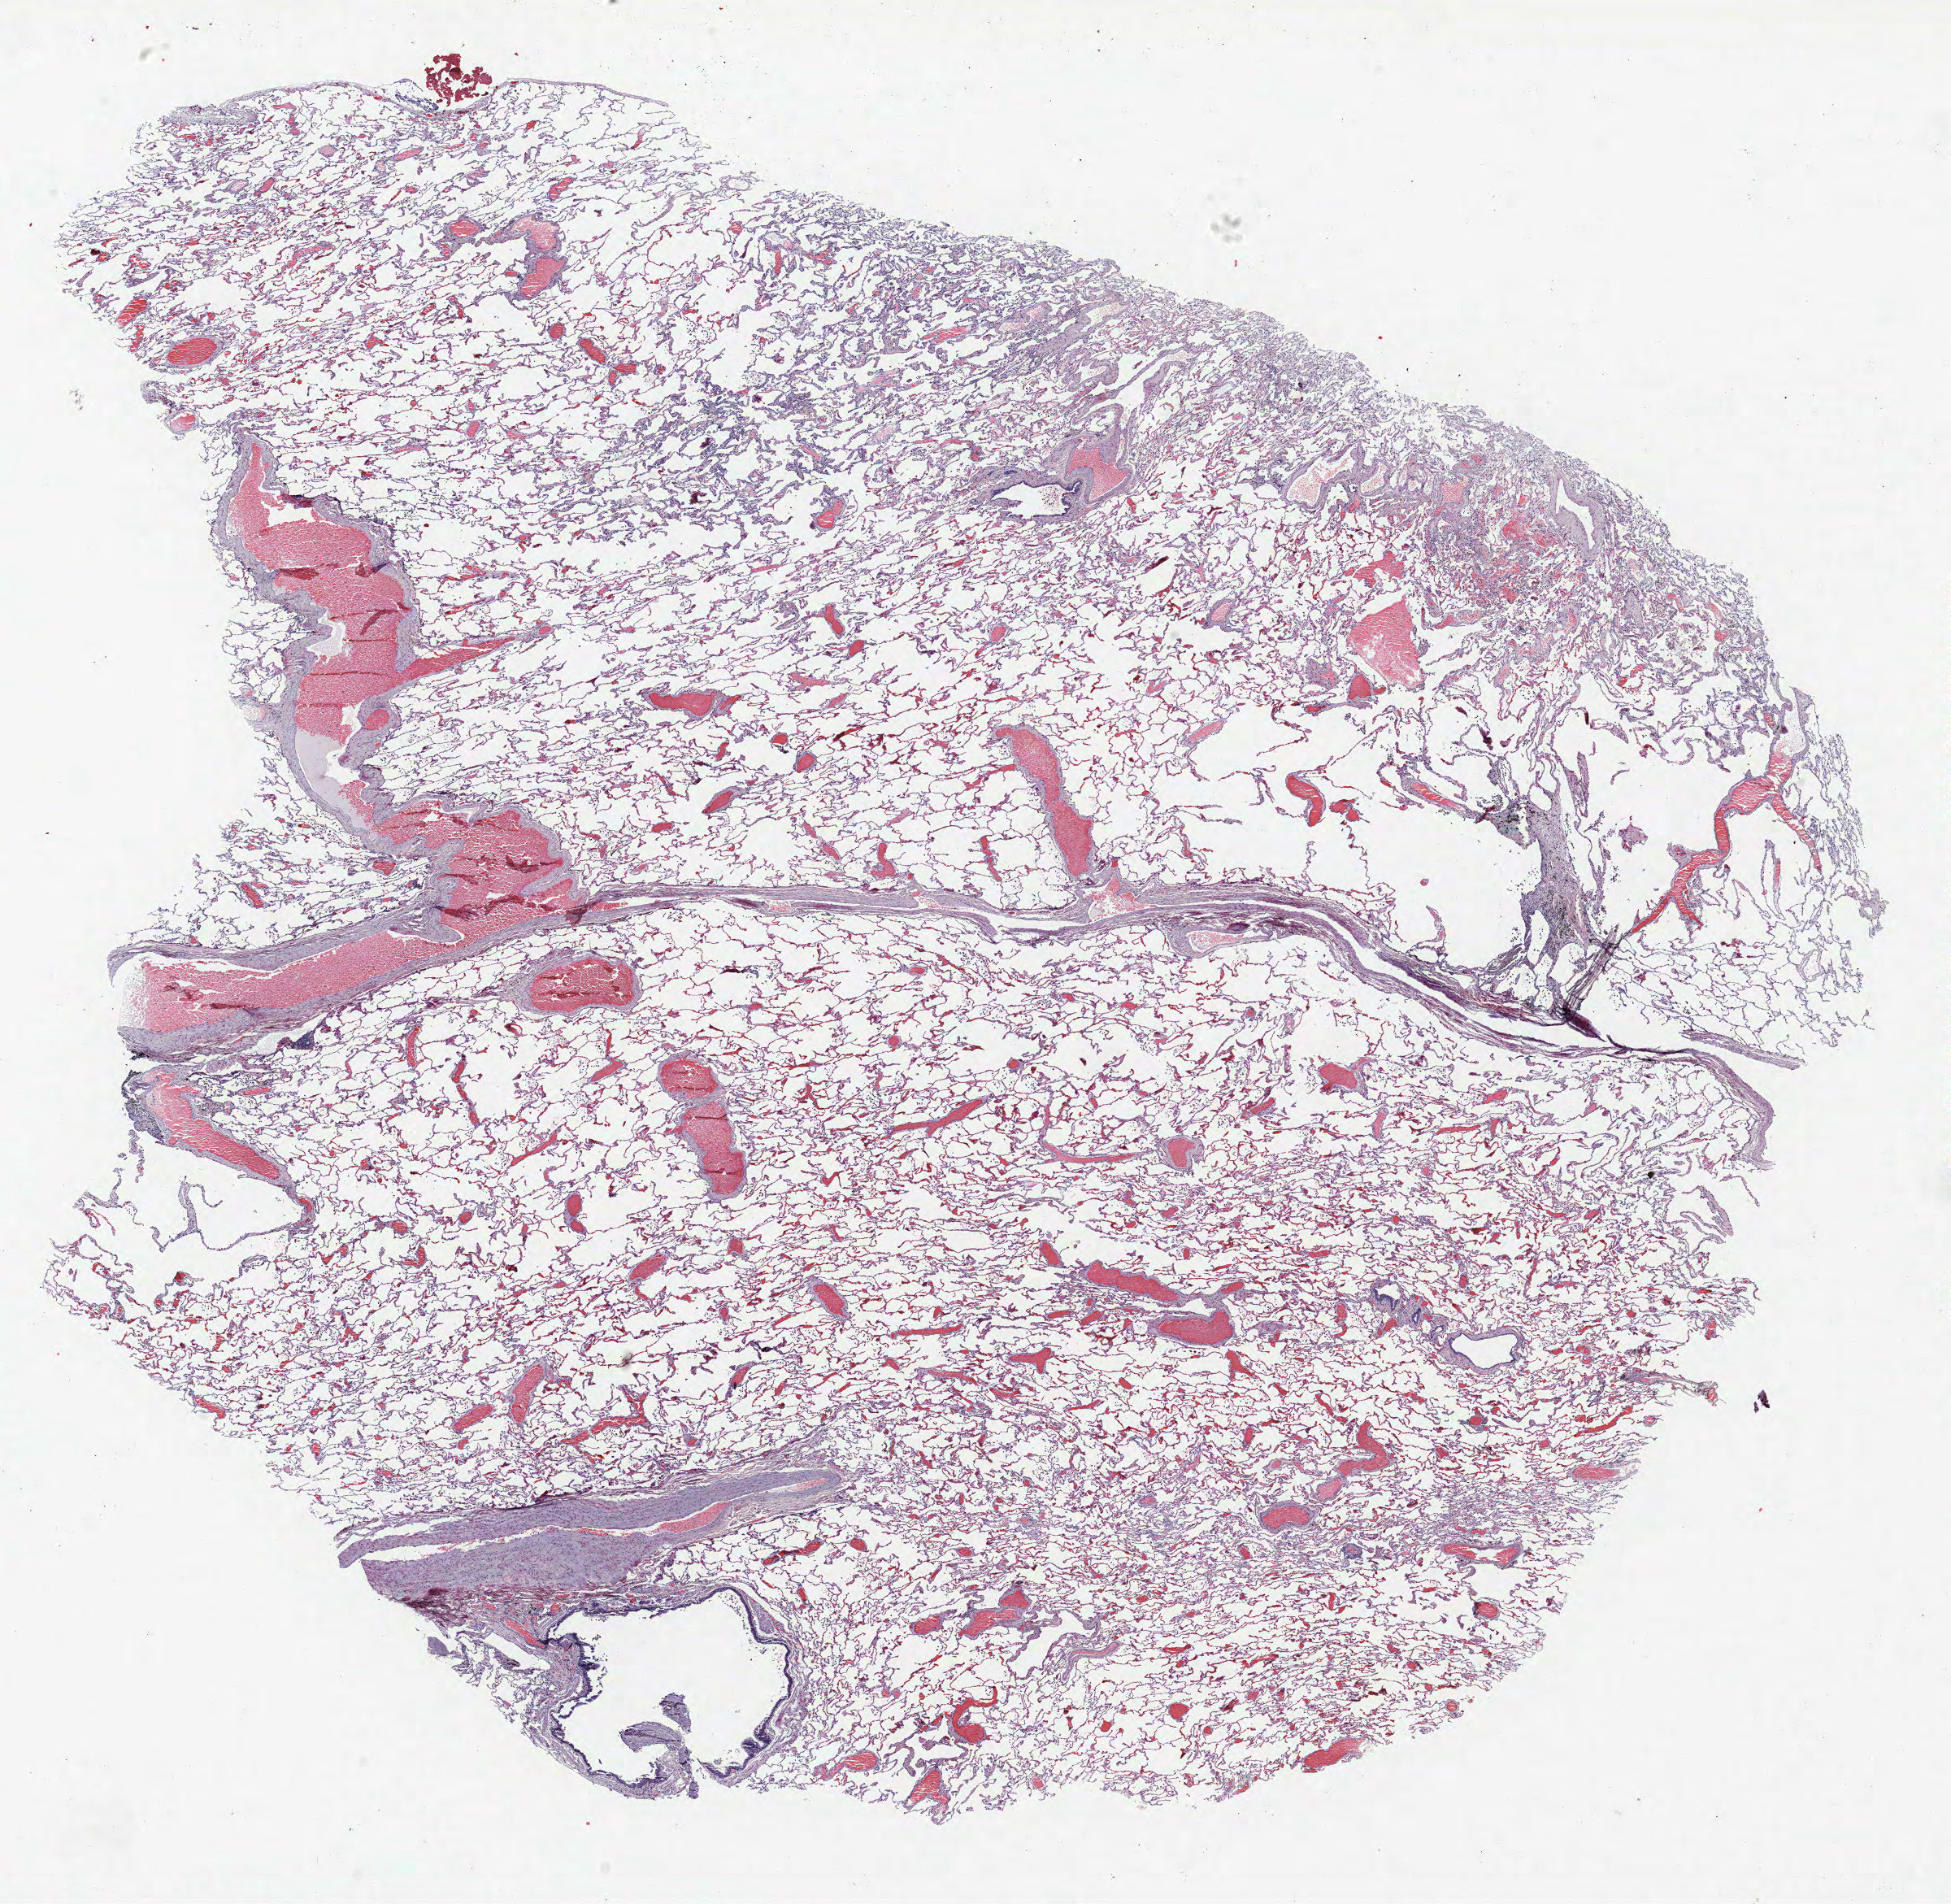
H&E whole-slide image, whole scanned area (about 19.2 x 18.7 mm) shown as a low-resolution overview. FFPE section. Lung tissue. Male patient, aged 68 at enrolment. Grade: well differentiated (G1).
* tumour size (pathology): 35 mm
* ICD-O-3 topography: upper lobe of lung (C34.1)
* primary tumour location (clinical record): right upper lobe, right lower lobe
* stage (AJCC 6th edition): IV
* participant's lung-cancer diagnosis: Adenocarcinoma, NOS